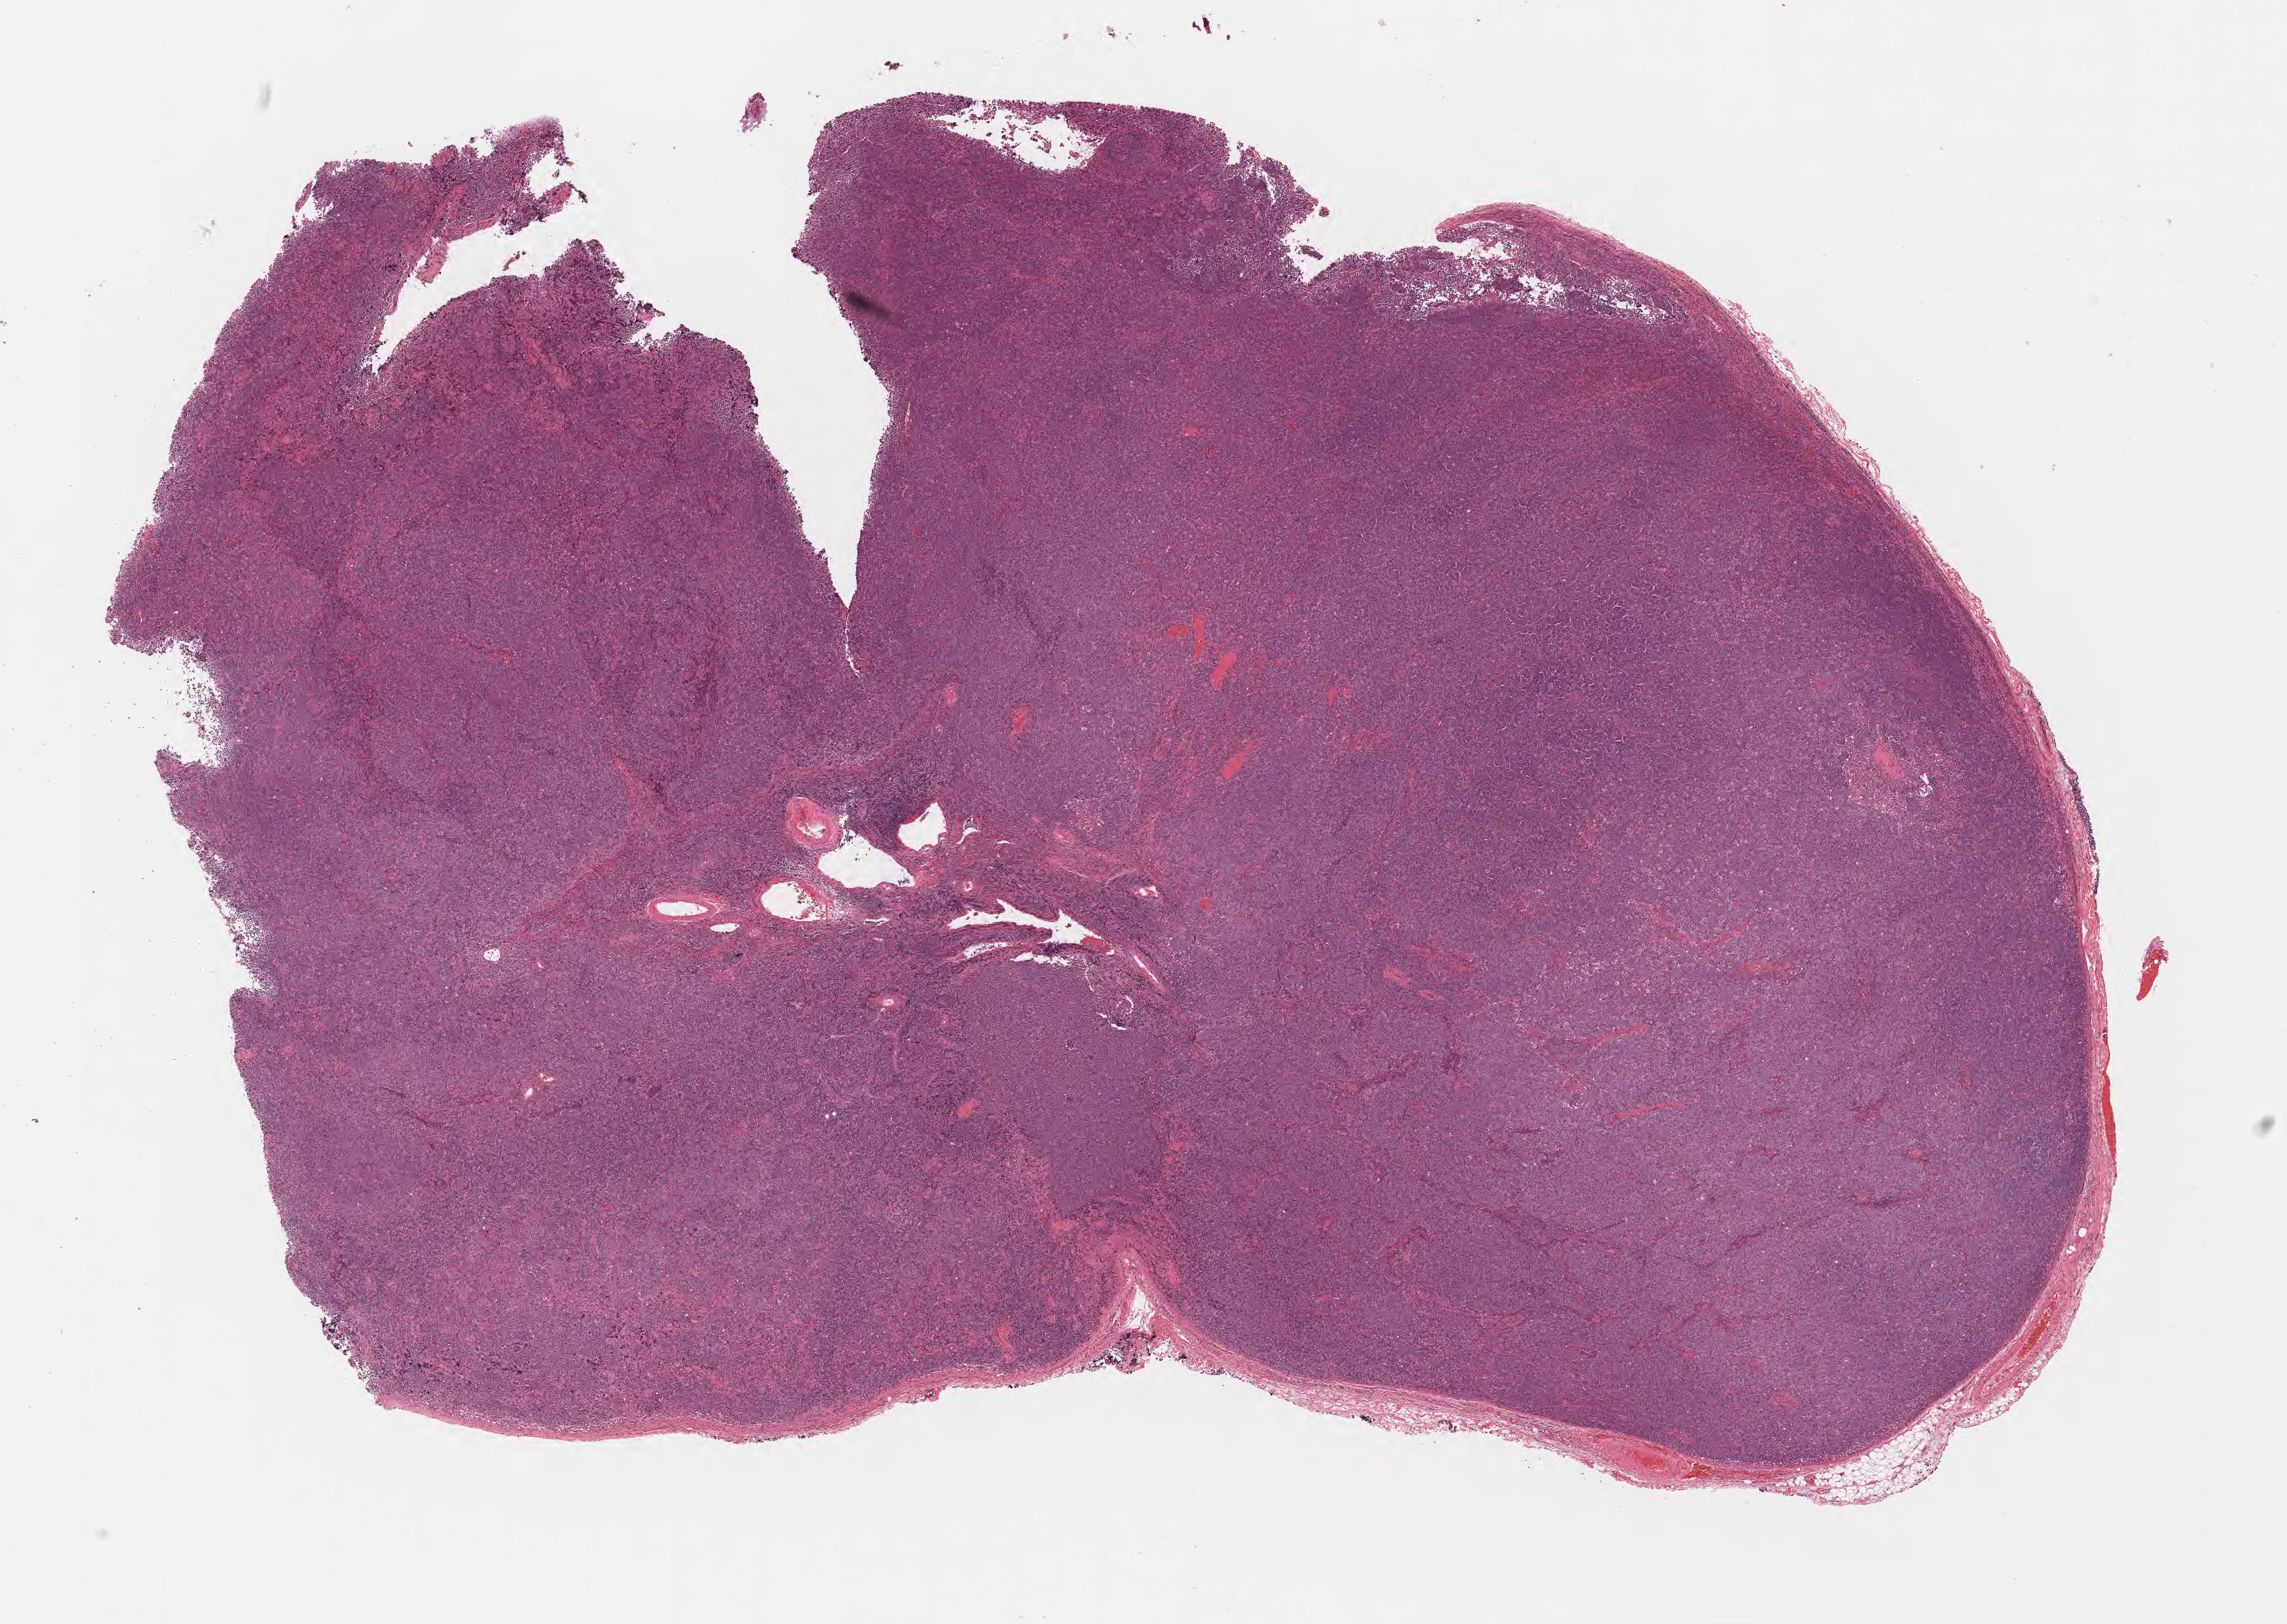
Whole-slide image, H&E stain, shown as a low-resolution overview of the whole scanned area (about 13.6 x 9.7 mm), specimen: tumor tissue, anatomic site: lymph node. Patient: male, age 32 years.
Histologic diagnosis: Diffuse large B-cell lymphoma, NOS.